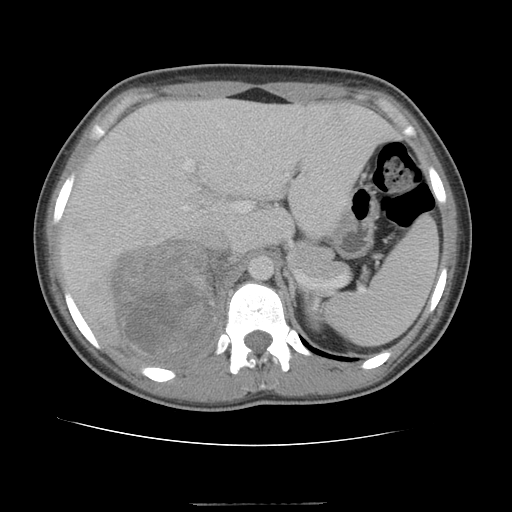
Contrast-enhanced abdominal CT, one axial slice; slice 76 of 100 in the series (ordered by position); intravenous contrast given; soft-tissue window (W 400 / L 40 HU); 5 mm slice thickness; 512 × 512 image matrix, field of view 360 × 360 mm. Female patient, age 21 years. From the clinical record (not read from this slice): diagnosis: adrenocortical carcinoma; tumour side: right adrenal; tumour size at pathology: 15.5 cm; Ki-67 index: 26 %; stage (as recorded): 3.
Outlined on this slice (semi-automatic segmentation, software-assisted and operator-edited):
- mass: bounding box [x1, y1, x2, y2] px = [114, 243, 221, 357]